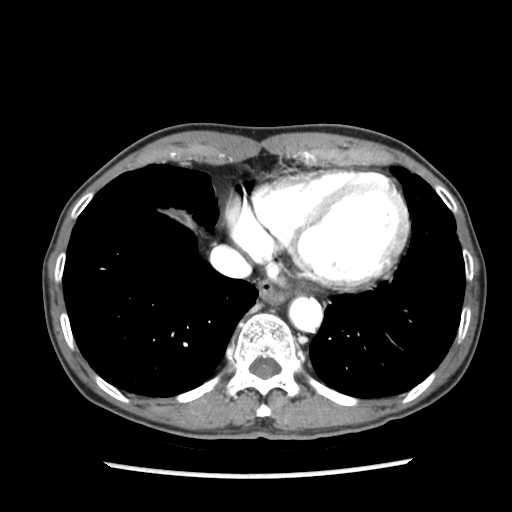
Contrast-enhanced abdominal CT (liver protocol), one axial slice; reconstruction kernel STANDARD; 140 kVp; soft-tissue window (W 400 / L 40 HU); 2.5 mm slice thickness; 512 × 512 image matrix, field of view 300 × 300 mm. Case-level facts recorded for this patient, not image findings: diagnosis: hepatocellular carcinoma (patient treated with transarterial chemoembolisation; whether this scan precedes or follows treatment is not stated here); TNM stage (as recorded): Stage-IIIB; Child-Pugh class: A; tumour differentiation: well differentiated; tumour nodularity: uninodular.
Annotated regions visible in this slice (semi-automatic segmentation, software-assisted and operator-edited):
- abdominal aorta: box from (x=290, y=299) to (x=321, y=330) px